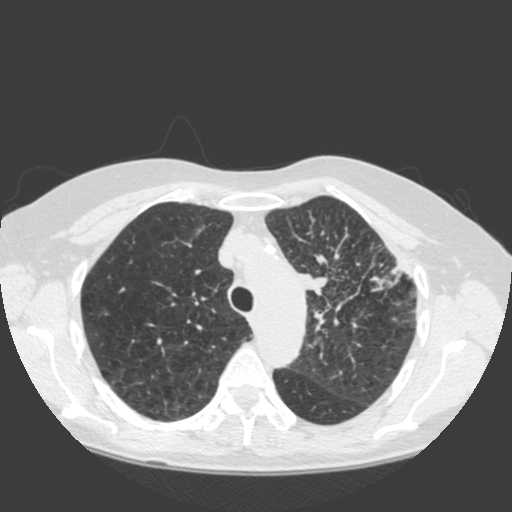
Low-dose screening chest CT, one axial slice; 120 kVp; lung window (W 1500 / L -600 HU); 512 × 512 image matrix, field of view 350 × 350 mm.
Outlined on this slice (manually delineated by an expert):
- lesion 1 (tumor, hilum of left lung): bounding box [x1, y1, x2, y2] px = [294, 271, 328, 295]